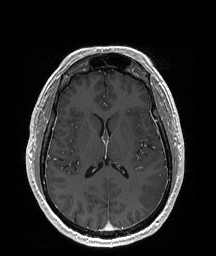
Brain MRI from a brain-tumour surgery series, one axial slice; position 91 of 192 along the scan axis; T1-weighted post-contrast; 1 mm slice thickness; 216 × 256 image matrix. Case-level facts recorded for this patient, not image findings: histopathology: Glioblastoma; WHO grade: 4; IDH mutation: no; tumour location: Left Temporal Parietal.
Annotated regions visible in this slice (outlined manually by an expert reader):
- tumour: box from (x=138, y=173) to (x=168, y=210) px